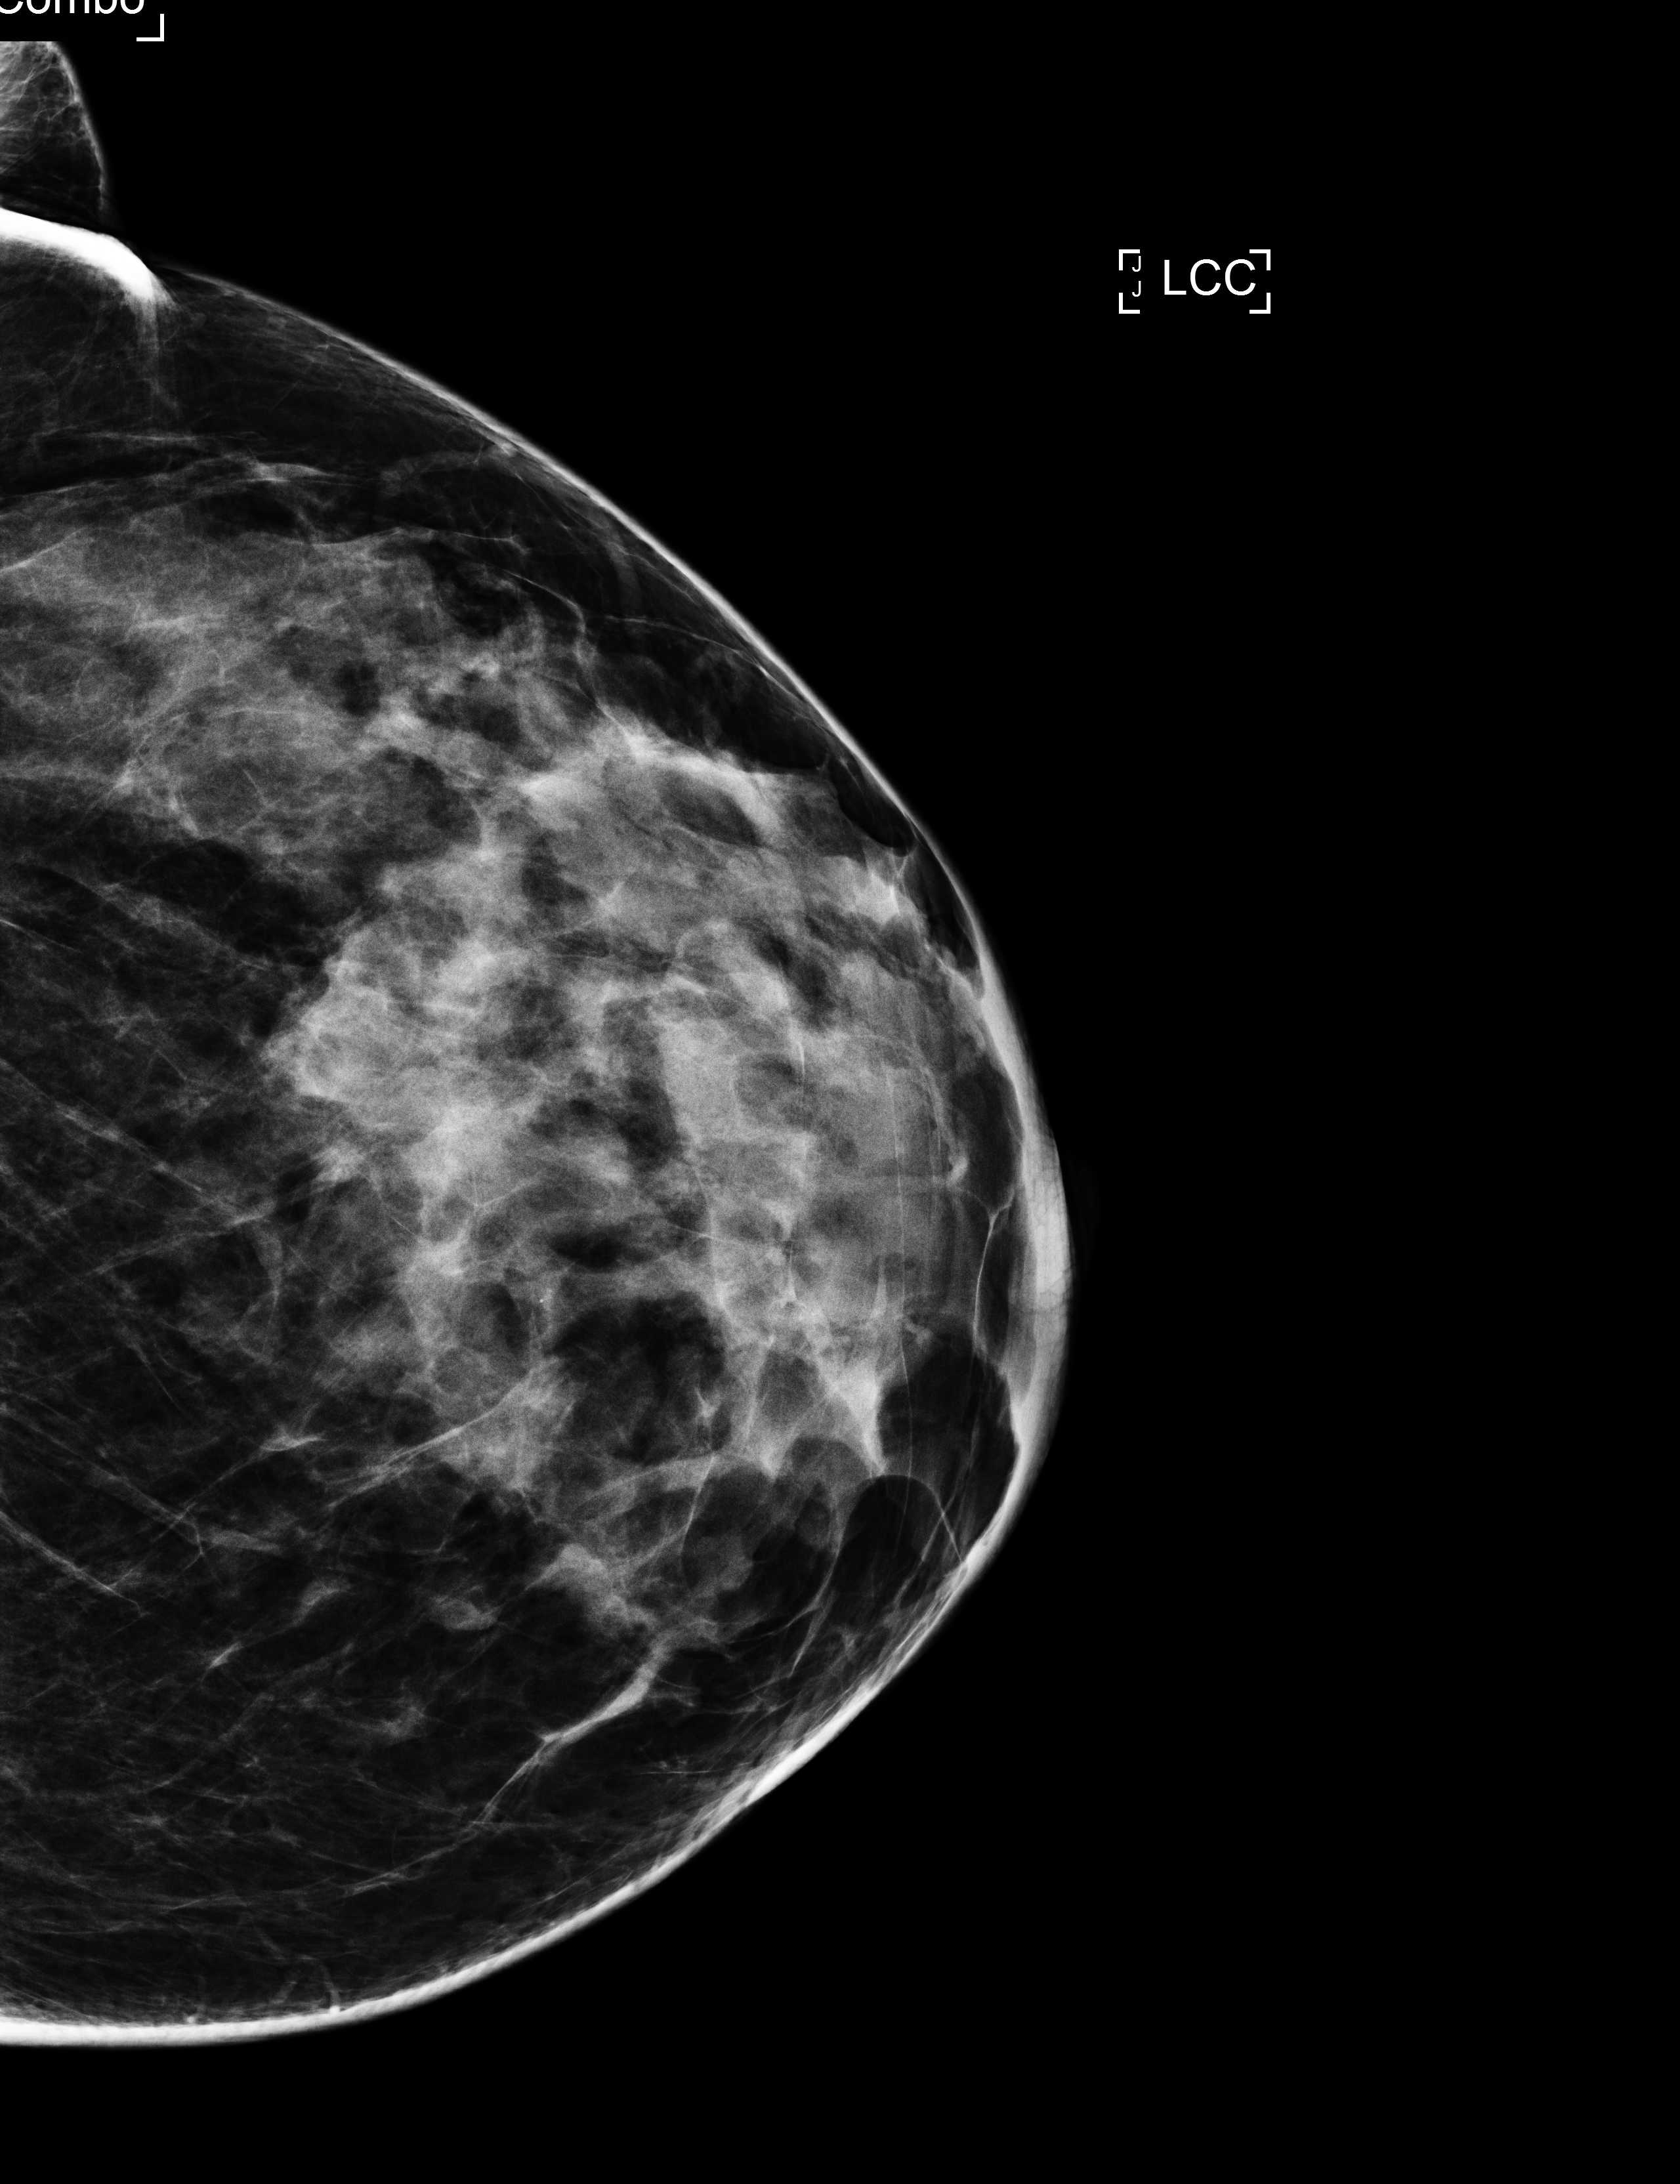
Digital mammogram (FFDM), left breast, cranio-caudal projection, annual screening mammography examination, compressed breast thickness 53 mm, system: Selenia Dimensions. Female patient, age 48 years.
Breast density at the screening exam (both breasts): heterogeneously dense (BI-RADS density category c). Final BI-RADS assessment for this screening round (tomosynthesis exam, both breasts): category 1. Recall: no recall after this screen.